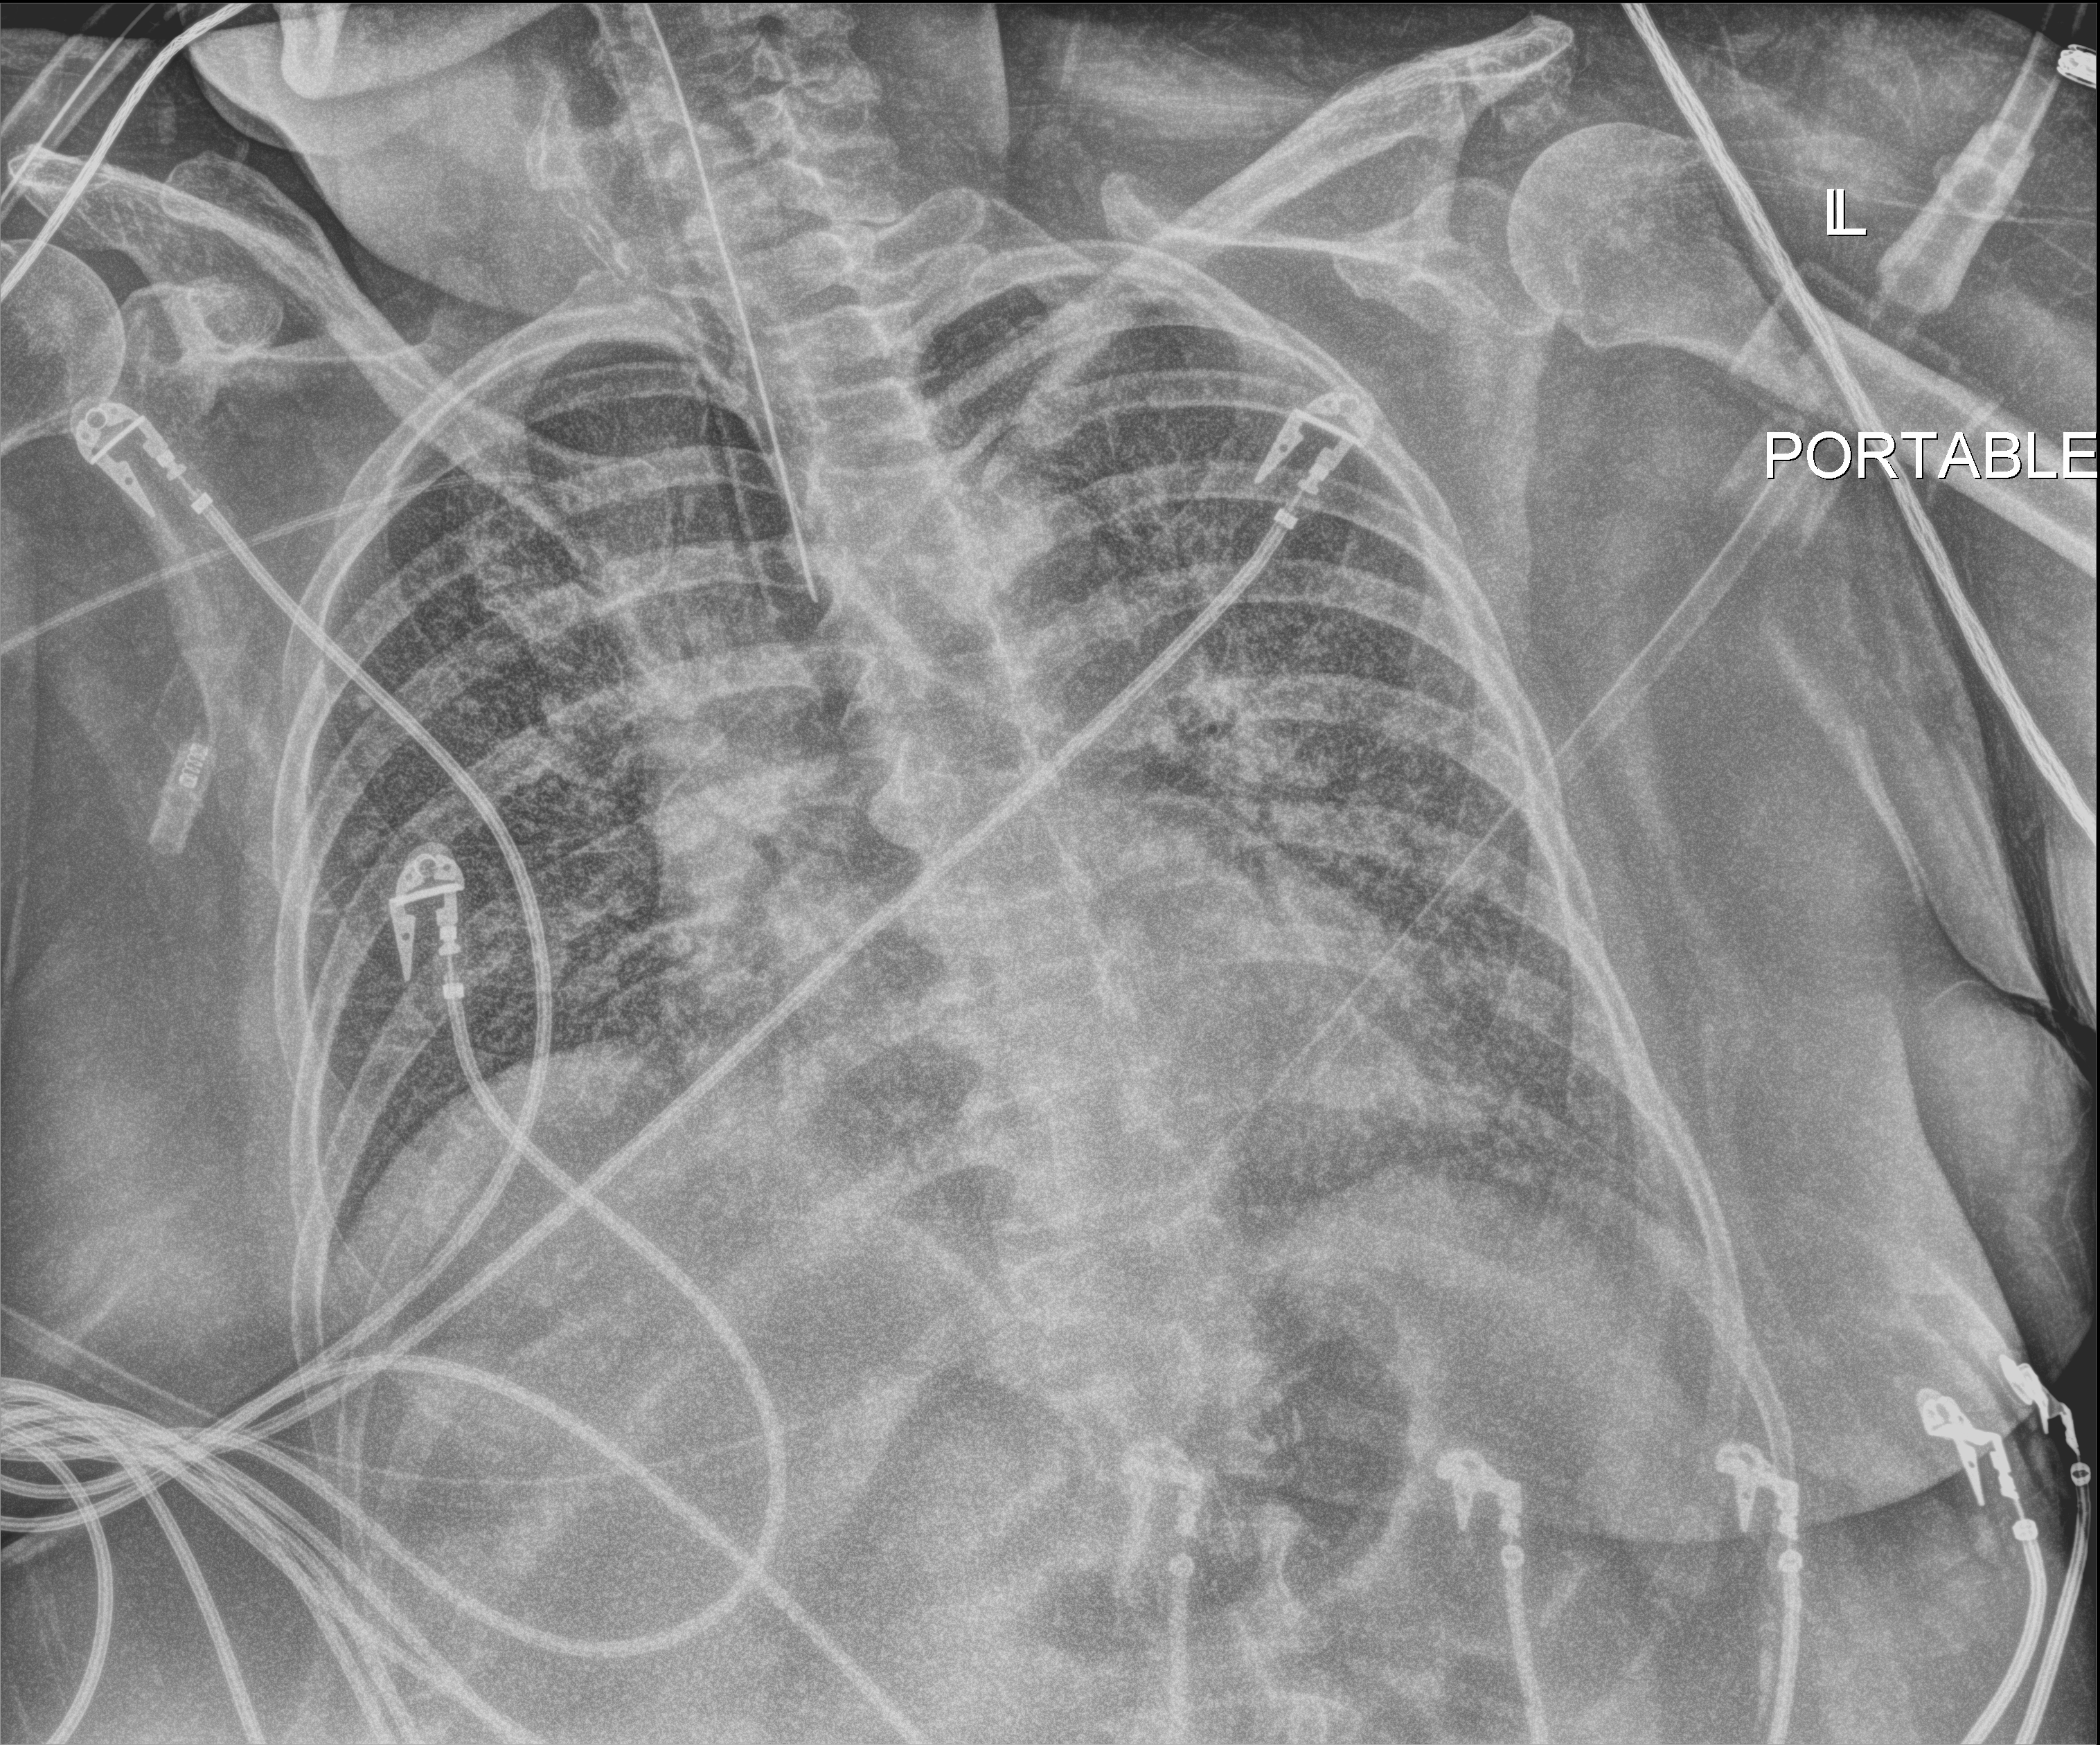
Bedside chest radiograph (digital radiography); anteroposterior (AP) projection. Patient hospitalised with COVID-19; female, aged 60–74 years.
From the hospital-stay record, not from the radiograph (when in the stay this image was taken is not recorded): admitted to intensive care during this hospital stay: yes.